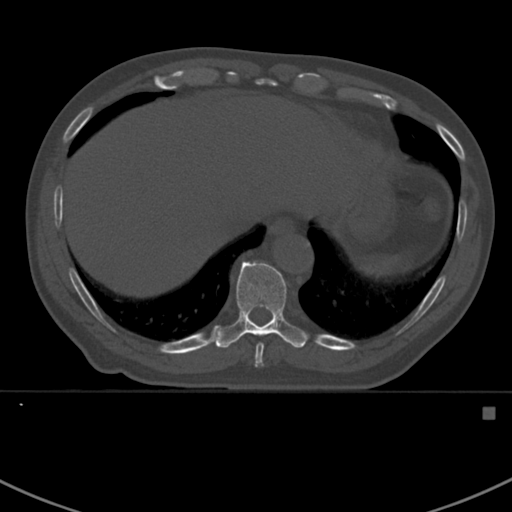
CT including the spine, one axial slice. Position 369 of 412 along the scan axis. Bone window (W 1800 / L 400 HU). 1.5 mm slice thickness. 512 × 512 image matrix, field of view 358 × 358 mm. Patient: male, 59 years. Case-level facts recorded for this patient, not image findings: primary cancer: prostate.
Structures marked on this image (semi-automatic segmentation, software-assisted and operator-edited):
- T10 vertebra: bounding box <214,261,308,367> (left, top, right, bottom; pixels)
- T9 vertebra: <255,343,264,366>